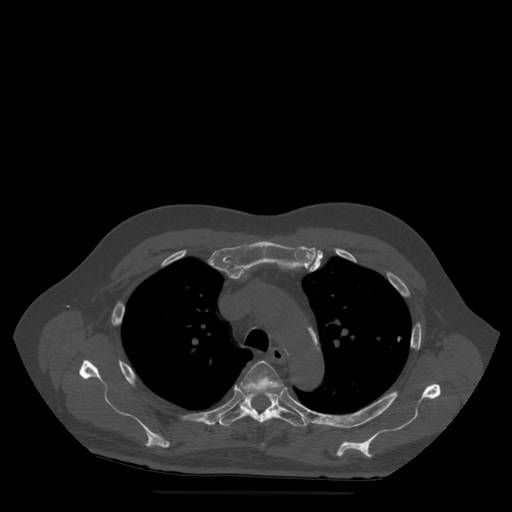
CT including the spine, one axial slice; position 381 of 522 along the scan axis; bone window (W 1800 / L 400 HU); 1.25 mm slice thickness; 512 × 512 image matrix. Patient age 72 years. From the clinical record (not read from this slice): primary cancer: prostate.
Annotated regions visible in this slice (semi-automatically segmented with operator editing):
- T4 vertebra: bounding box <241,361,284,396> (left, top, right, bottom; pixels)
- T5 vertebra: <219,391,308,427>